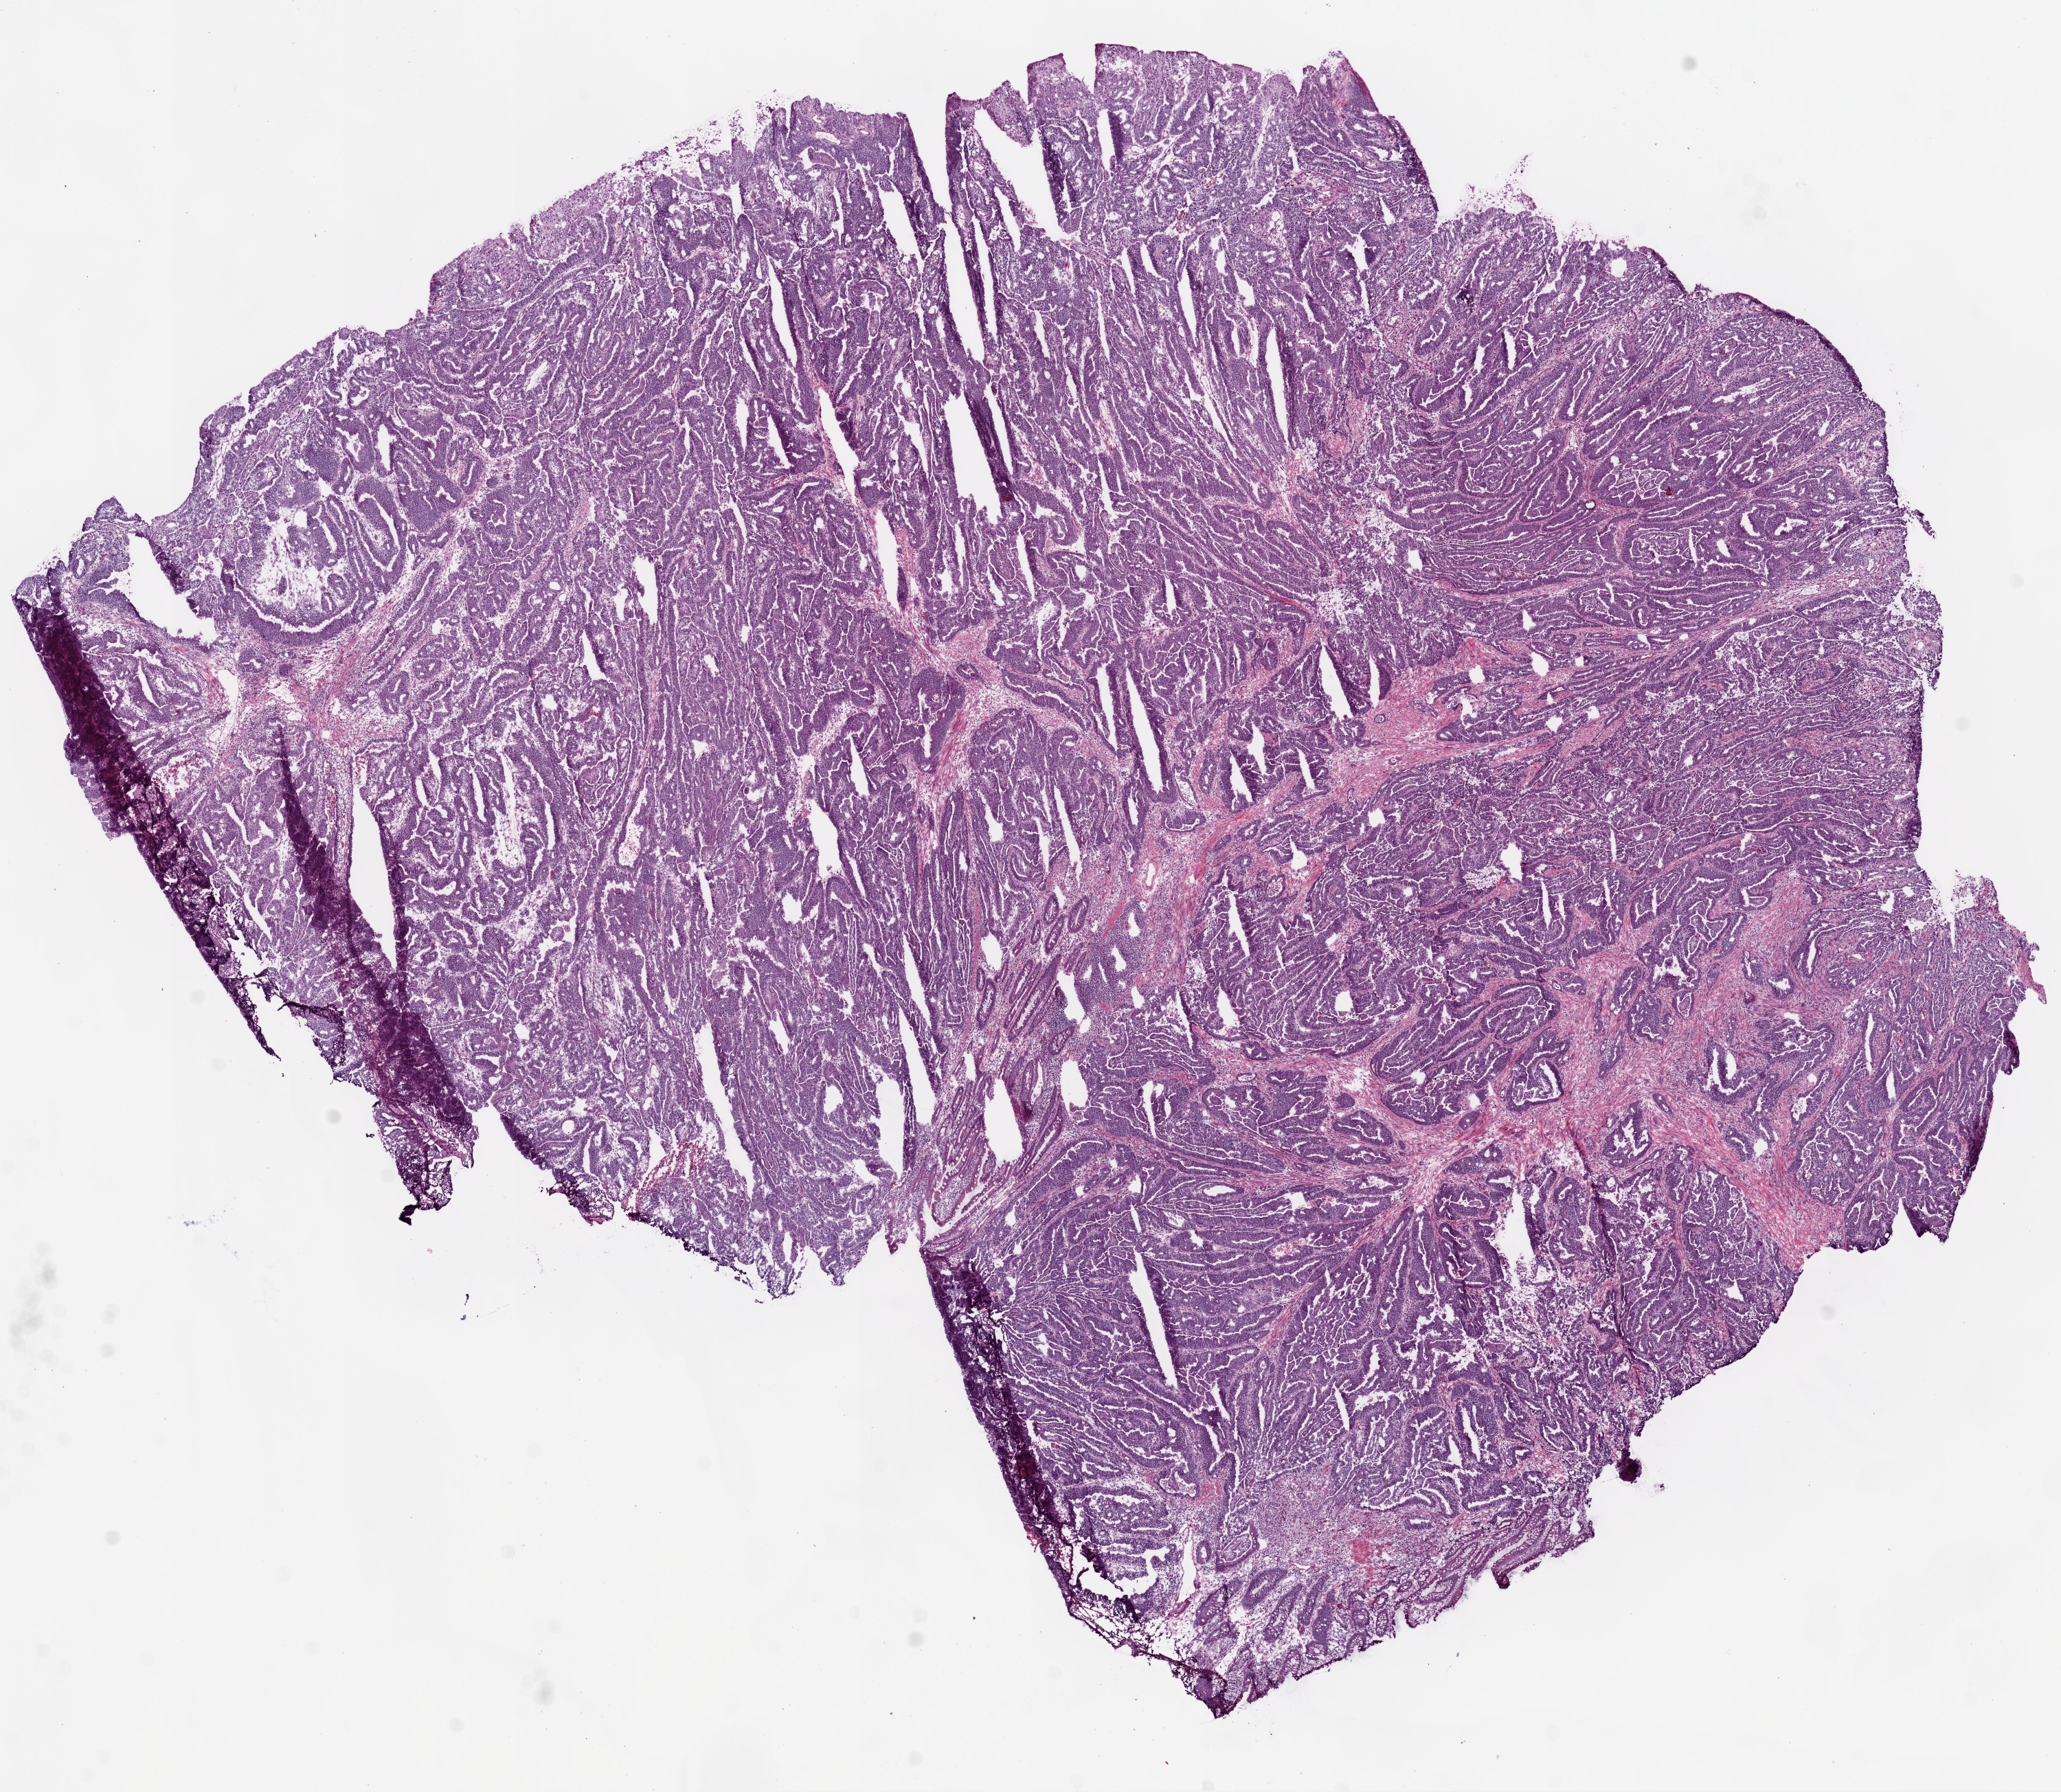
Whole-slide histology image, Hematoxylin and eosin (H&E) stained, shown as a low-resolution overview of the whole scanned area (about 12.0 x 10.5 mm, acquisition: 20x scan), frozen section from the bottom of the tissue portion, primary tumour sample from the colon. Patient: female, age at initial diagnosis 74 years. Pathologist review of this section (percent, as recorded): tumour cells 100%, tumour nuclei 80%, normal cells 0%, stromal cells 0%, necrosis 0%. Inflammatory infiltration, as recorded: lymphocyte infiltration 40%, monocyte infiltration 5%, neutrophil infiltration 50%.
* TNM: T3 N0 M0
* AJCC pathologic stage: II (5th edition)
* diagnosis: Adenocarcinoma, NOS (ascending colon)